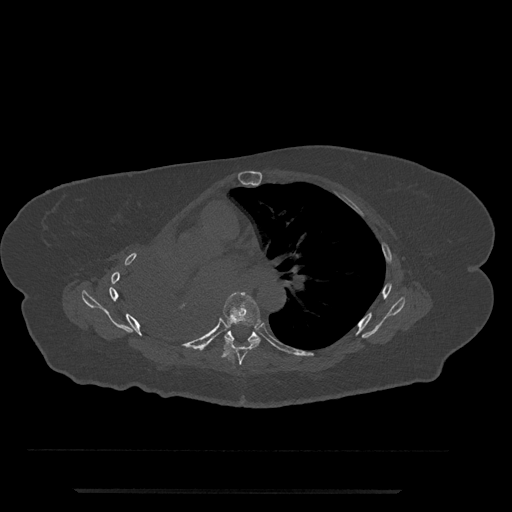
CT including the spine, one axial slice; position 474 of 797 along the scan axis; reconstruction kernel Br40s/3; 120 kVp; bone window (W 1800 / L 400 HU); 512 × 512 image matrix, field of view 440 × 440 mm. Female patient, age 51 years. From the clinical record (not read from this slice): primary cancer: neuro.
Outlined on this slice (semi-automatically segmented with operator editing):
- T6 vertebra: bounding box (x1, y1, x2, y2) in pixels: (223, 292, 261, 365)
- T7 vertebra: (224, 330, 289, 347)